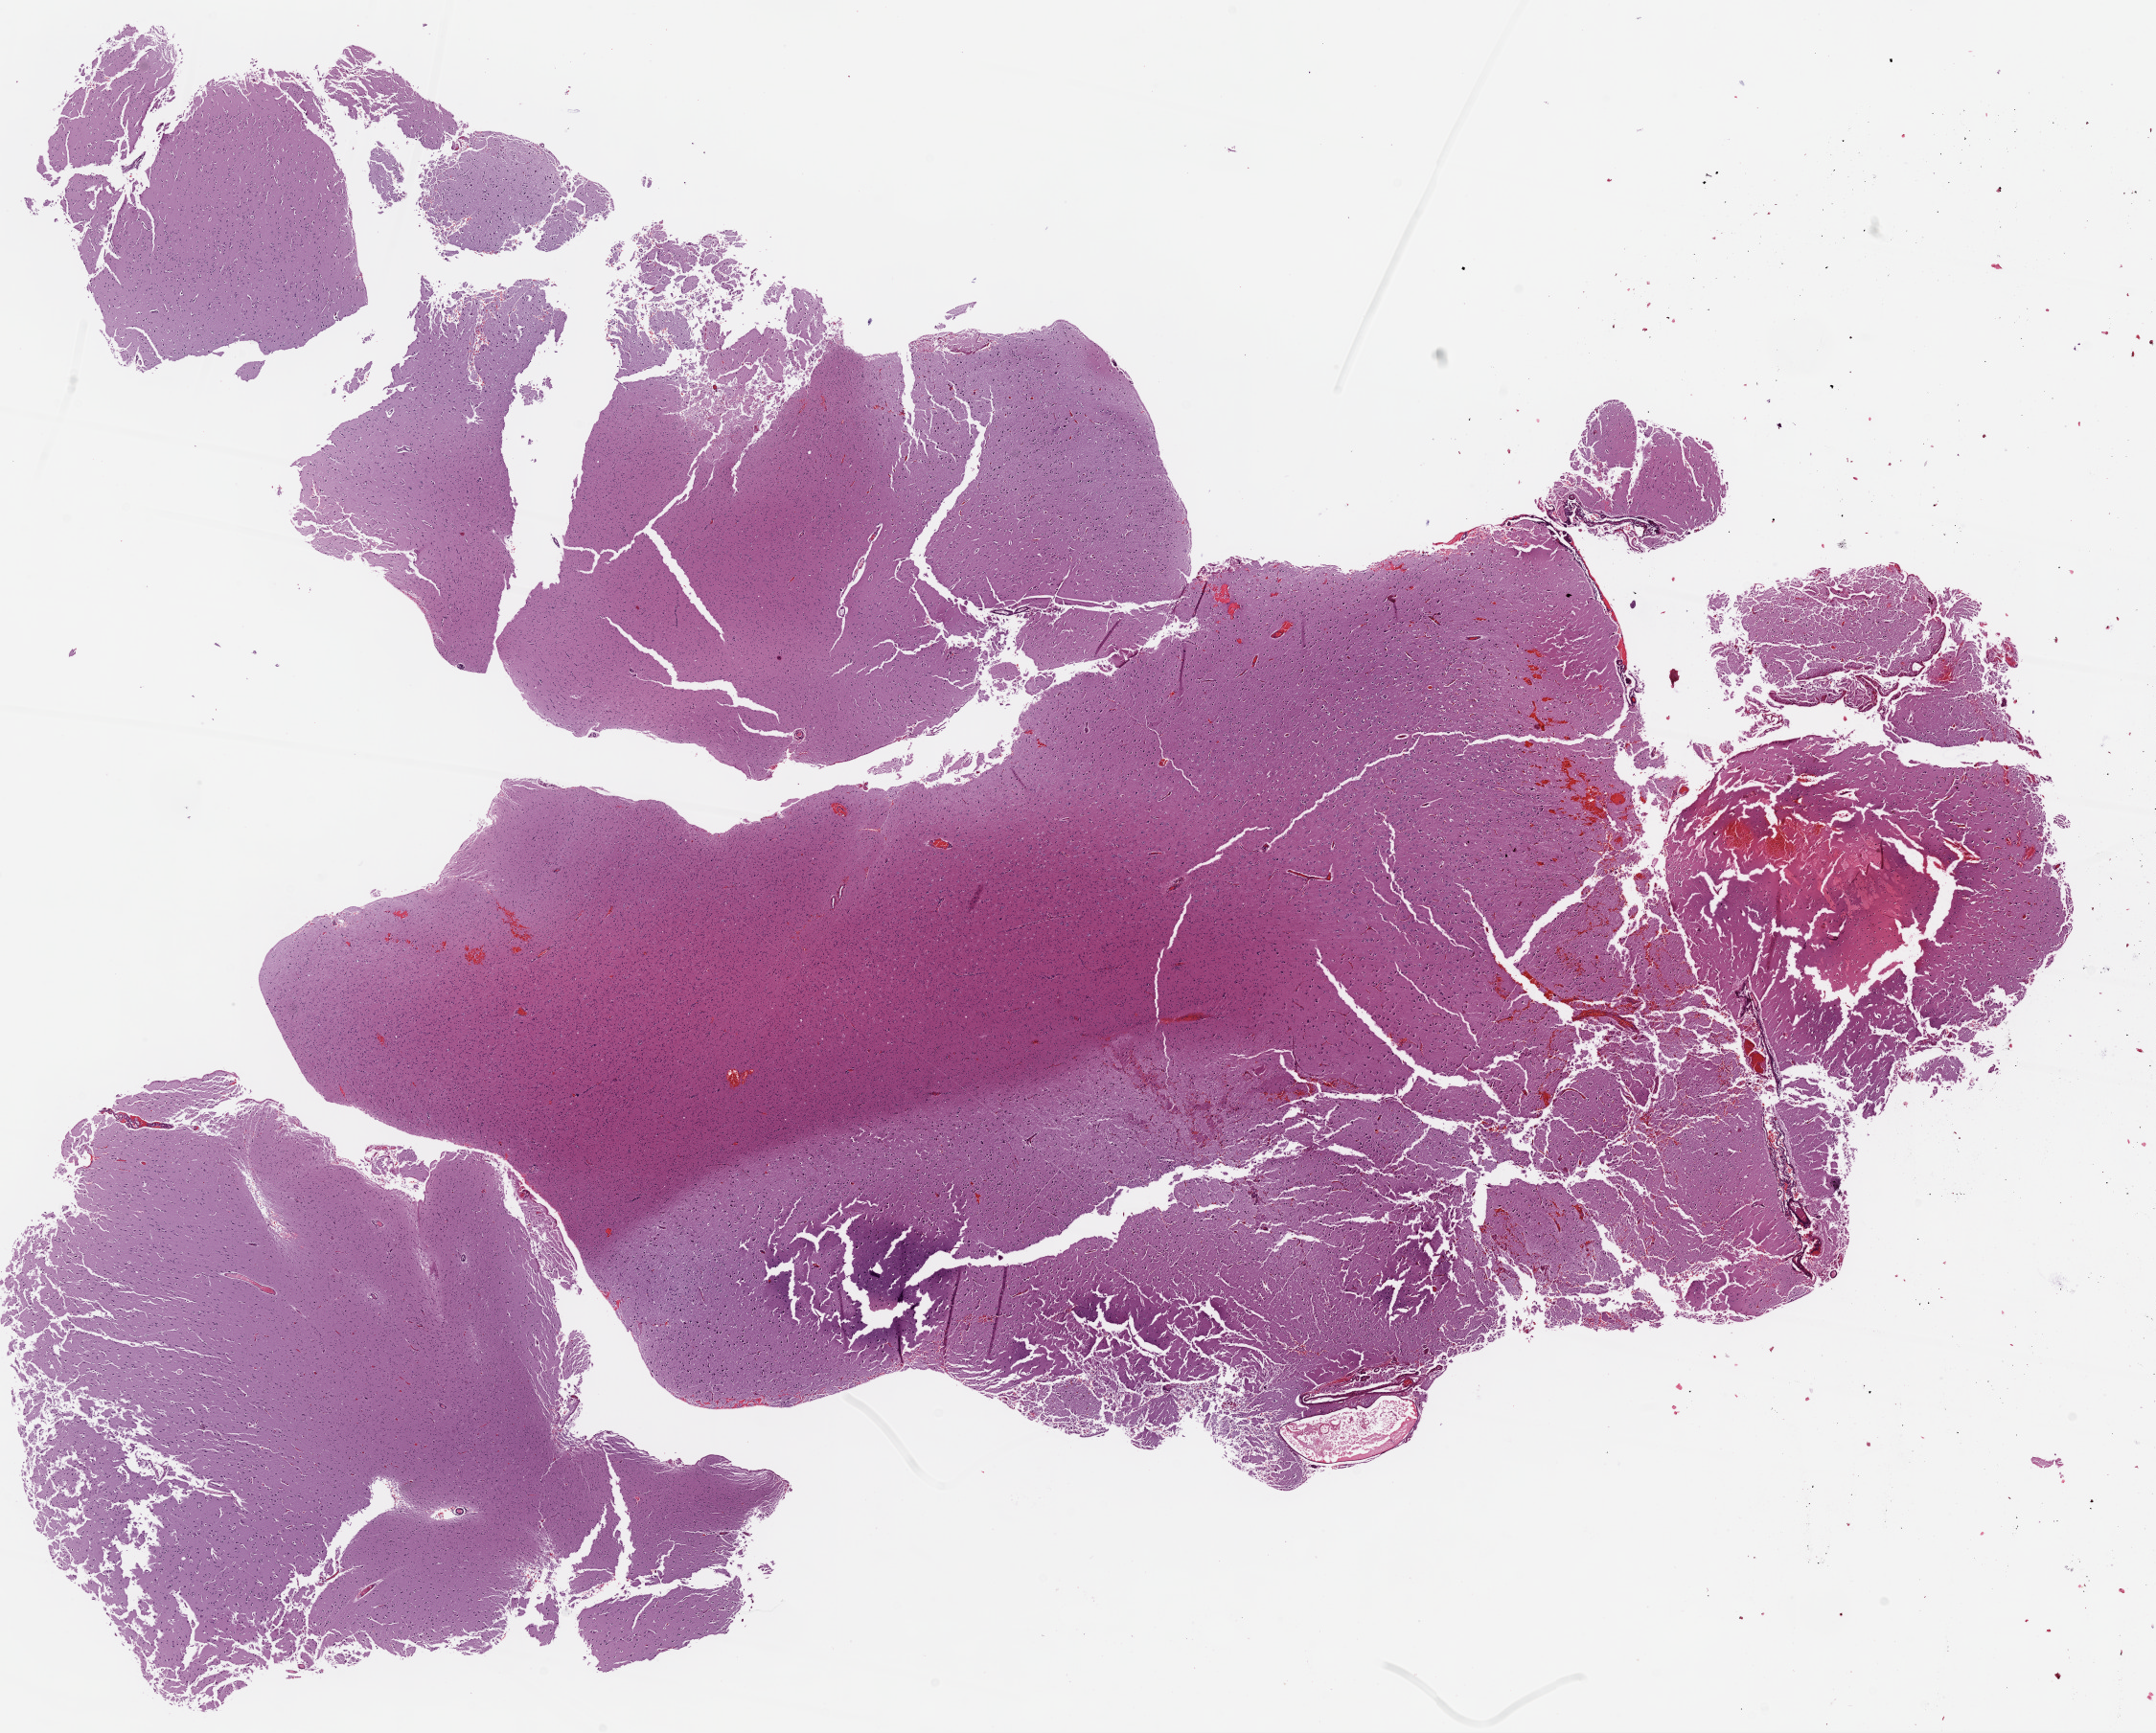
Whole-slide histology image, H&E — a low-resolution overview of the entire scanned area, about 18.1 x 14.5 mm. FFPE section. Brain, primary tumour sample. Patient: female, age at initial diagnosis 43 years.
Histologic diagnosis: Glioblastoma.